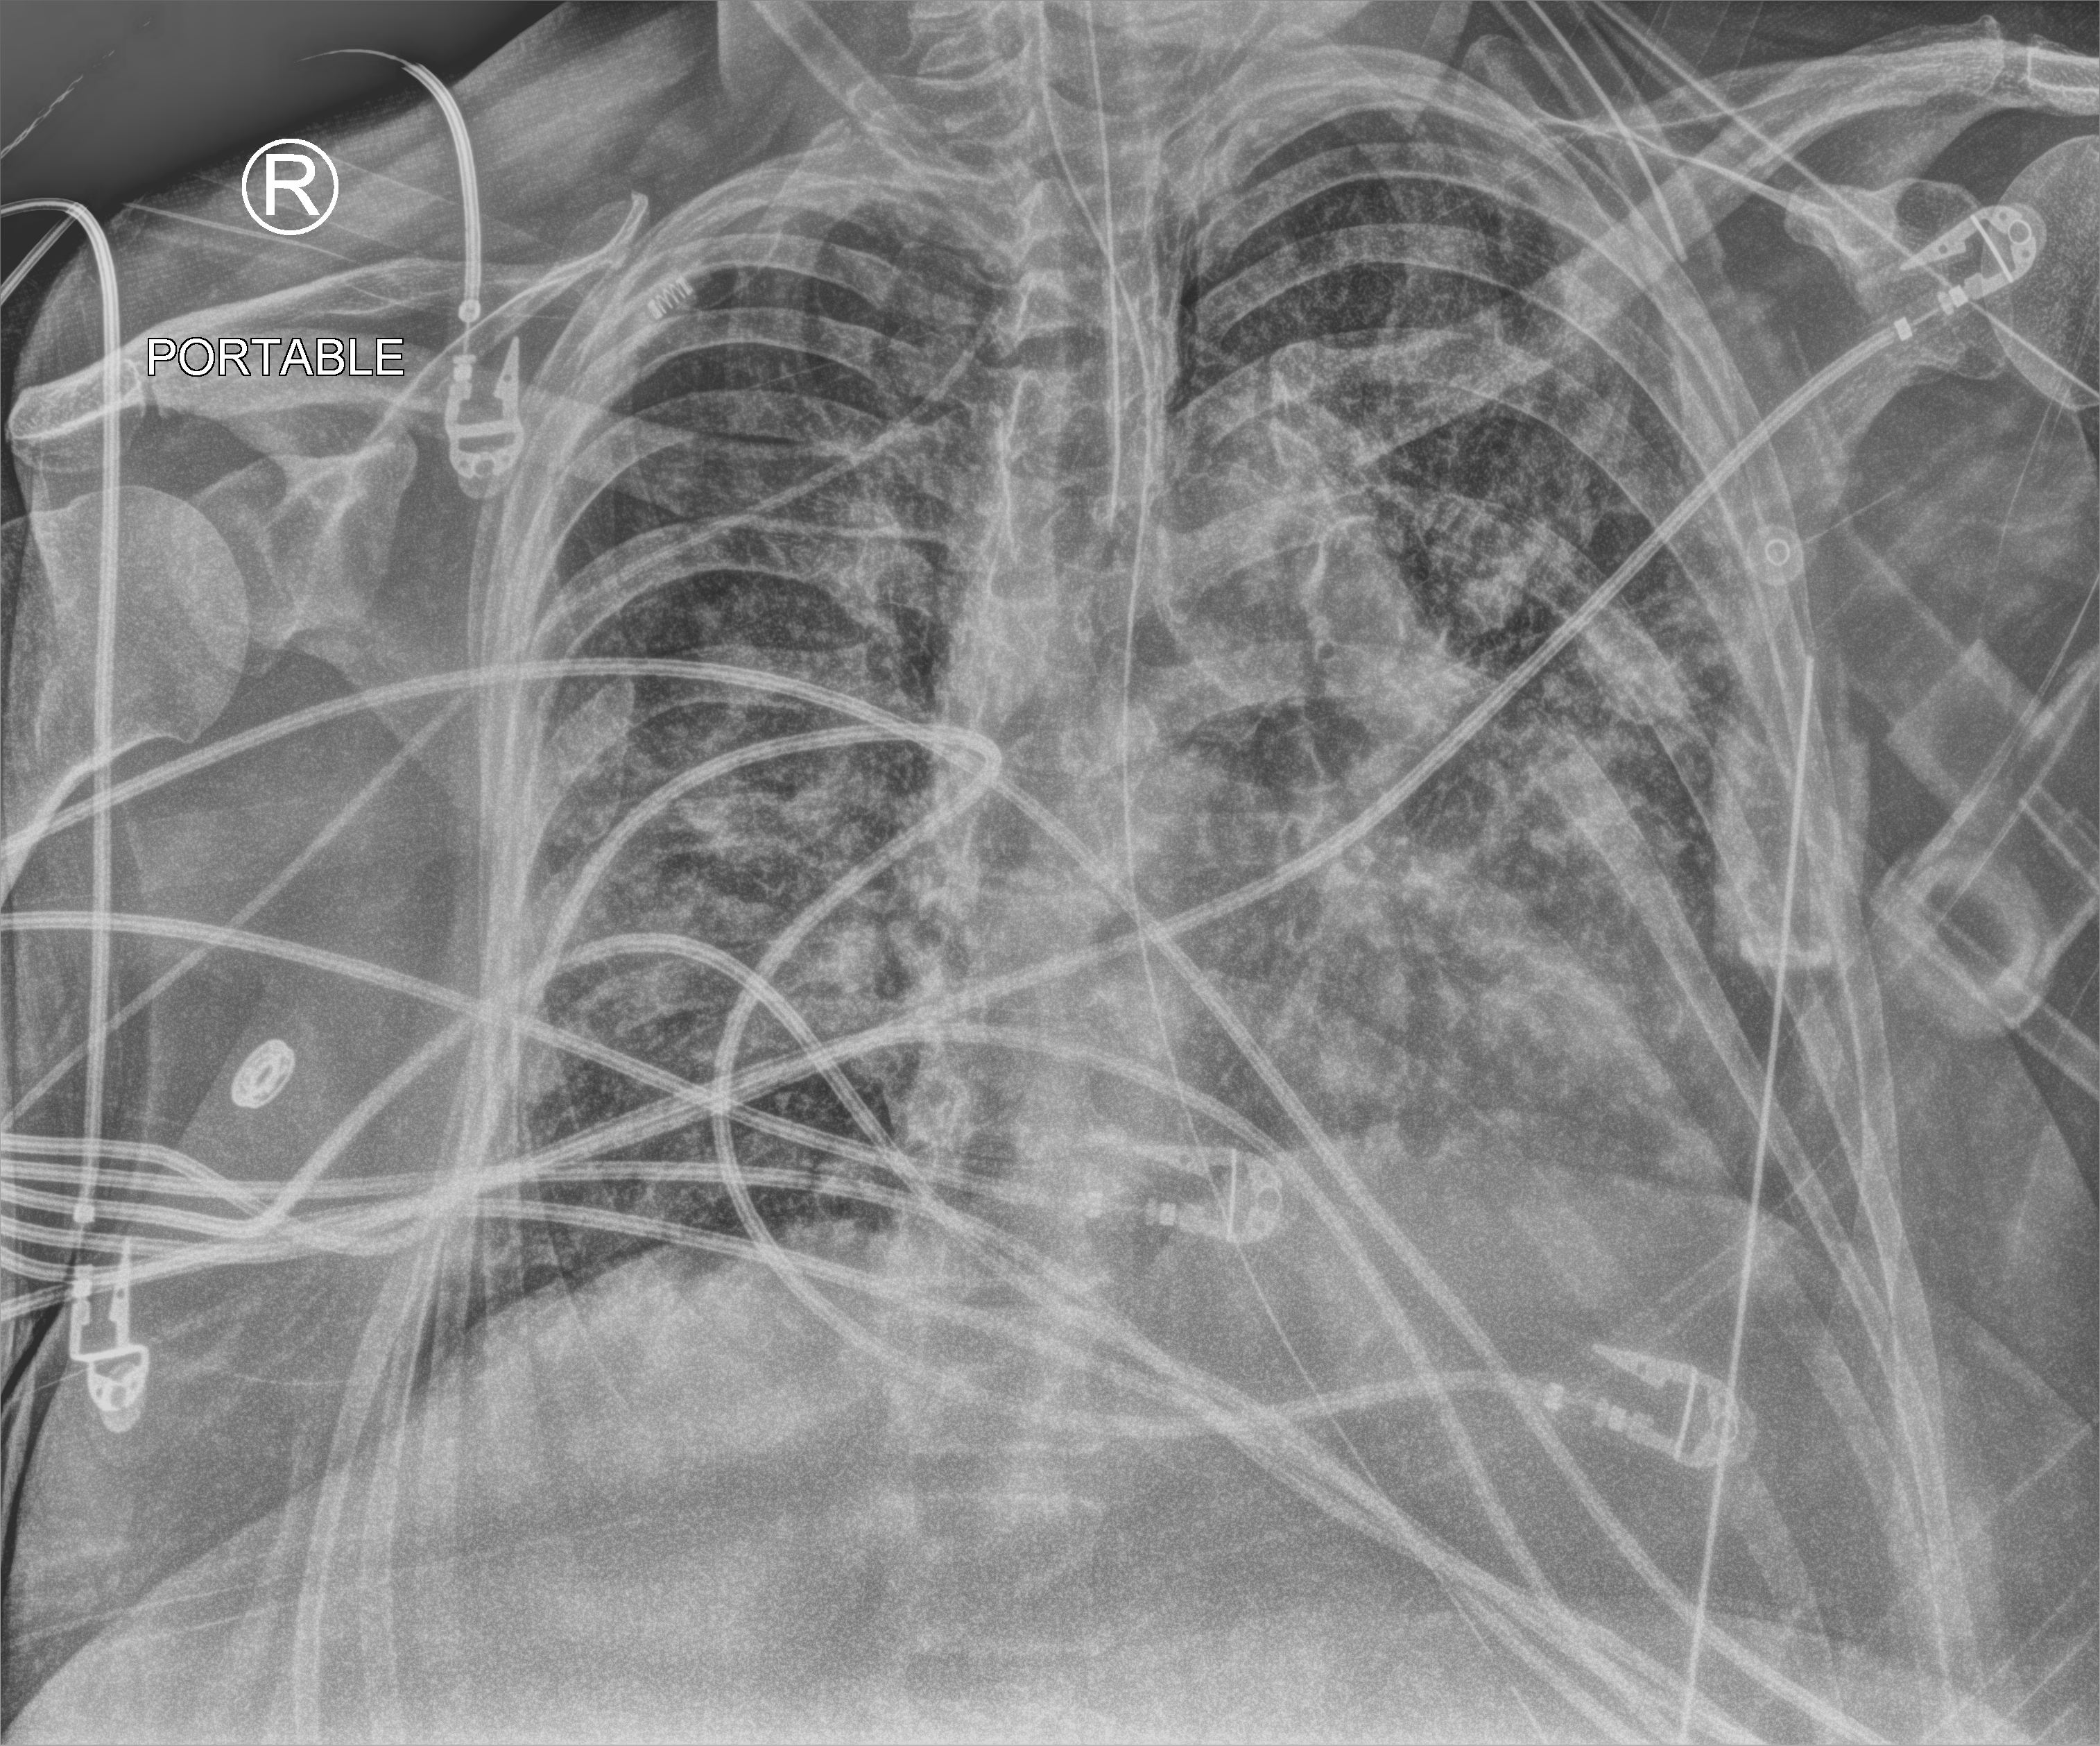
Chest X-ray (portable); anteroposterior (AP) projection. Patient hospitalised with COVID-19; female, aged 60–74 years.
From the hospital-stay record, not from the radiograph (when in the stay this image was taken is not recorded): mechanically ventilated during this hospital stay: yes; other chronic lung disease (admission record): yes.